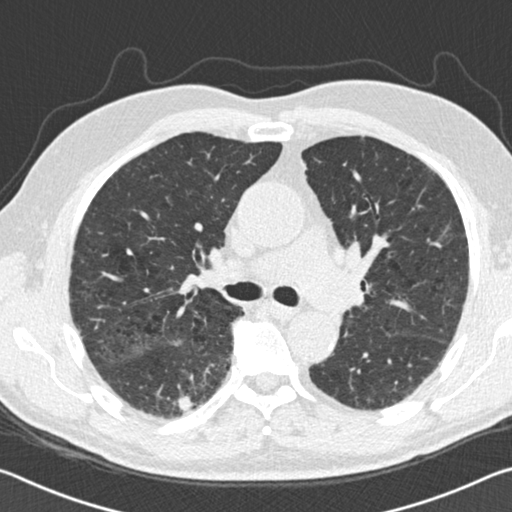
Axial slice from a low-dose chest CT screening exam. Second screening round (one year after baseline). Lung window (W 1500 / L -600 HU). 2 mm slice thickness. Standard (soft-tissue) reconstruction kernel (B30f). Slice 58 of 142 in the series. Male, age 69 years at enrolment. Current smoker at enrolment.
Lesion marked by an expert reader, bounding box [x1, y1, x2, y2] px = [160, 377, 208, 425]. Reader record for this screening exam (exam-level; its link to the box is not recorded): non-calcified nodule or mass ≥4 mm, right lower lobe, 10 × 10 mm, spiculated (stellate) margins, soft tissue attenuation, pre-existing on the prior screen: yes; interval growth: yes. Later outcome: lung cancer diagnosed 290 days after this screen — squamous cell carcinoma, NOS, right lower lobe, moderately differentiated (G2), stage IA (AJCC 6th edition), 25 mm at pathology.